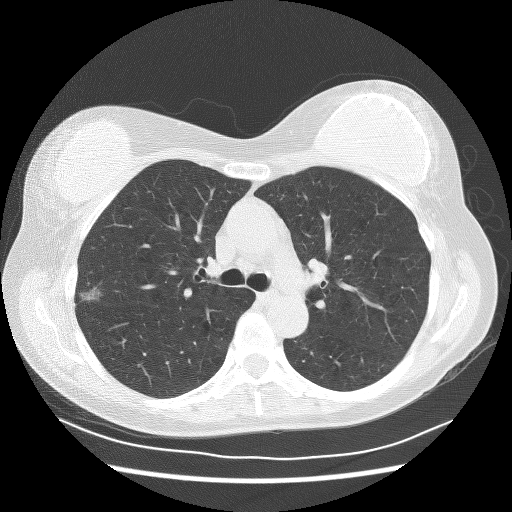
Axial slice from a low-dose chest CT screening exam, first (baseline) screen, lung window (W 1500 / L -600 HU), 2.5 mm slice thickness, 120 kVp, 512 × 512 image matrix. Female participant, aged 58 years at enrolment. Former smoker at enrolment.
Expert-annotated lung lesion, bounding box (x1, y1, x2, y2) in pixels: (64, 272, 115, 312). The screening reader recorded 2 non-calcified nodules or masses ≥4 mm on this exam; which of them this box marks is not recorded. Lung cancer was diagnosed 510 days after this screen: bronchiolo-alveolar adenocarcinoma, NOS, right upper lobe, well differentiated (G1), stage IA (AJCC 6th edition).